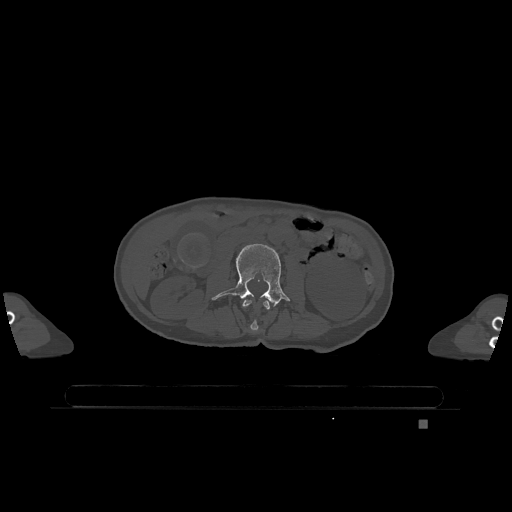
CT including the spine, one axial slice. Position 366 of 1317 along the scan axis. Bone window (W 1800 / L 400 HU). 0.5 mm slice thickness. 512 × 512 image matrix, field of view 500 × 500 mm. Patient: female, 74 years. From the clinical record (not read from this slice): primary cancer: lung; vertebrae with lytic lesions (as recorded): T1, T4, T5, T6, L4, L5.
Annotated regions visible in this slice (semi-automatically segmented with operator editing):
- L2 vertebra: bounding box (x1, y1, x2, y2) in pixels: (242, 299, 270, 332)
- L3 vertebra: (212, 244, 290, 307)